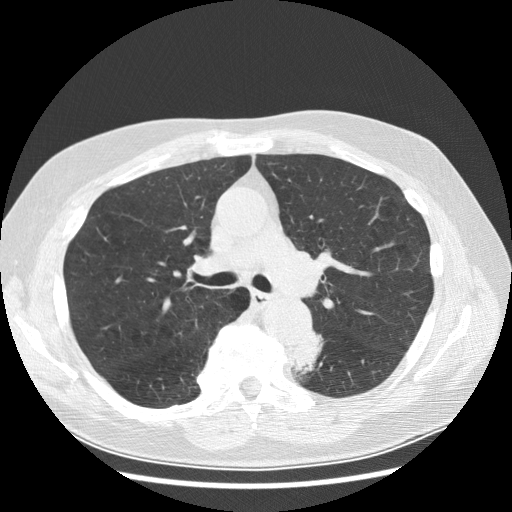
Low-dose screening chest CT, one axial slice; 120 kVp; lung window (W 1500 / L -600 HU); 2.5 mm slice thickness; 512 × 512 image matrix.
Outlined on this slice (outlined manually by an expert reader):
- lesion 1 (tumor, lower lobe of left lung): box from (x=292, y=328) to (x=324, y=375) px